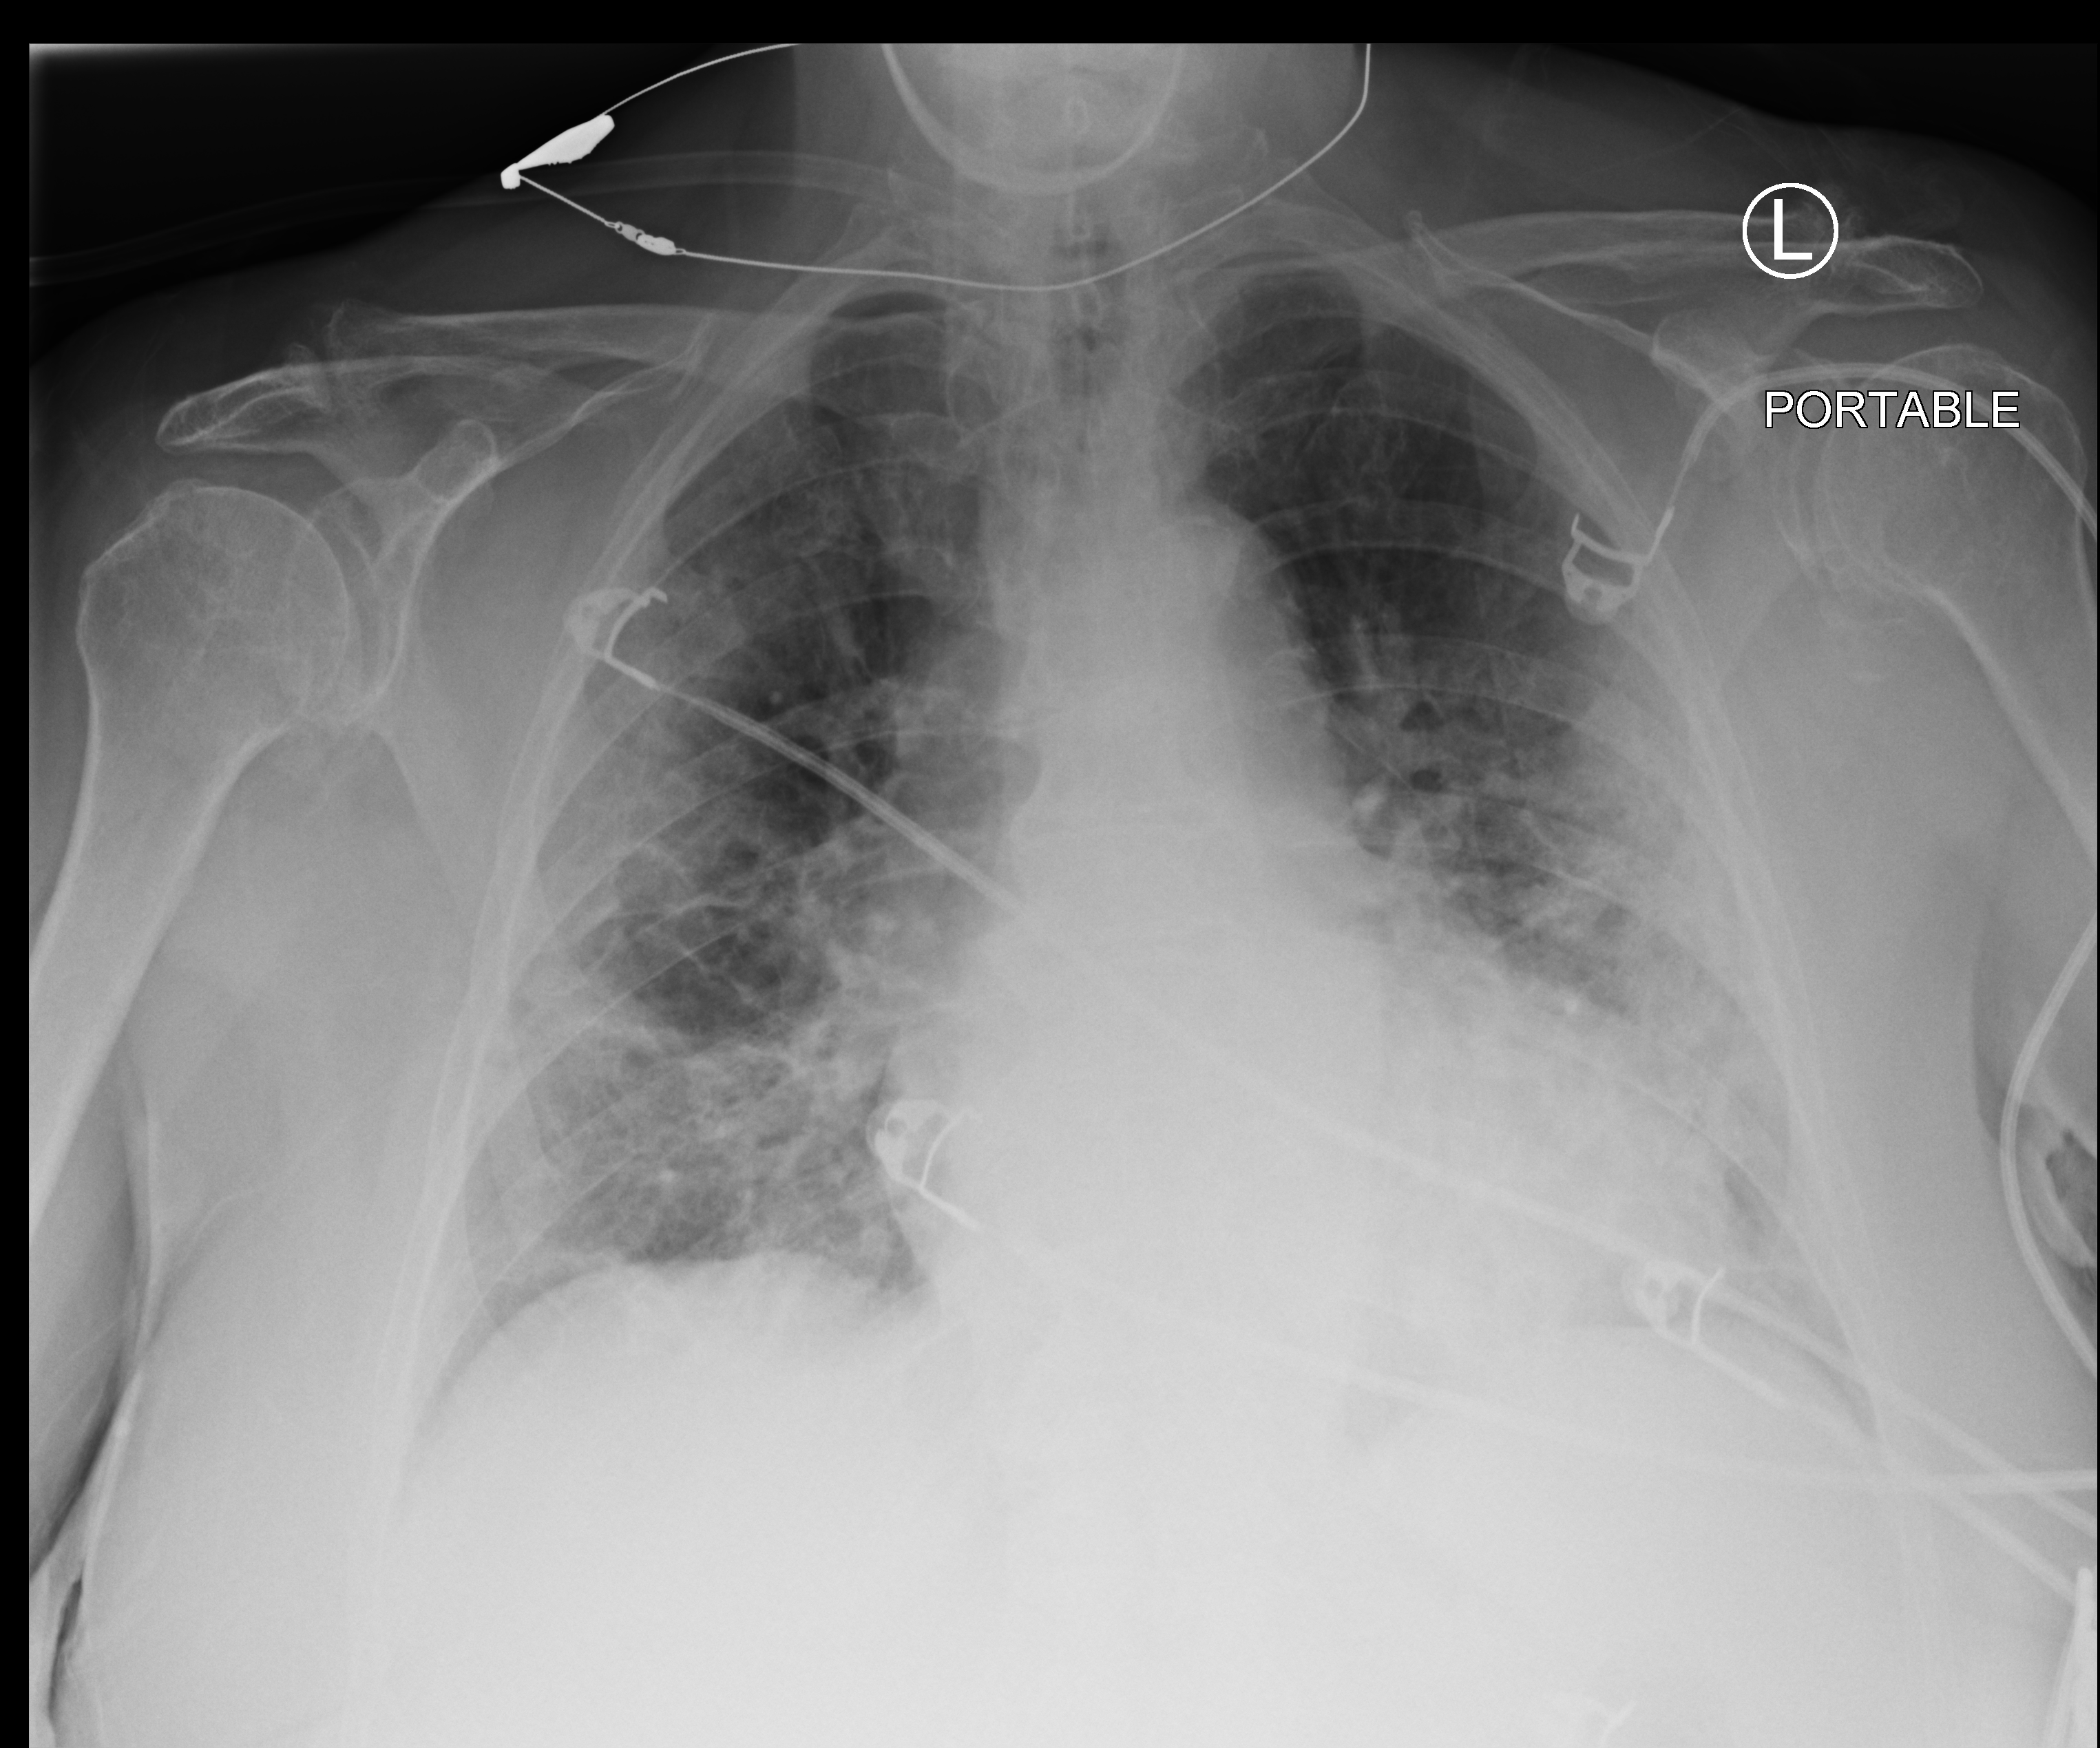
Bedside chest radiograph (computed radiography); anteroposterior (AP) projection. Patient hospitalised with COVID-19; female, aged 75–90 years.
Hospital-stay facts (about this admission, not read from this image; timing relative to this image not recorded):
- admitted to intensive care during this hospital stay: no